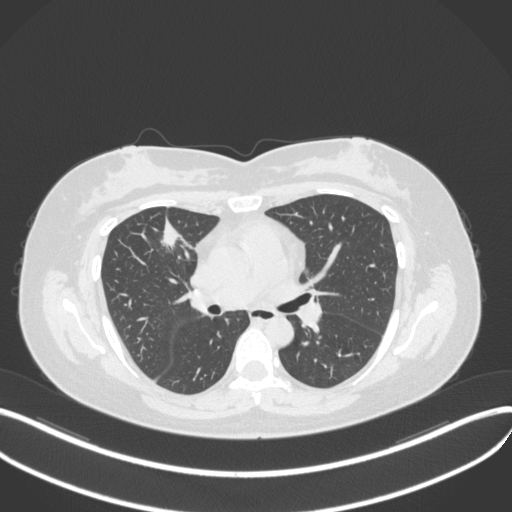
Chest CT, one axial slice. Position 182 of 272 along the scan axis. Reconstruction kernel B31f. 120 kVp. Lung window (W 1500 / L -600 HU). 1 mm slice thickness. 512 × 512 image matrix, field of view 400 × 400 mm. Female patient, age 42 years. Case-level facts recorded for this patient, not image findings: clinical TNM (as recorded): T1b N0 M0.
Outlined on this slice (bounding box drawn by a radiologist):
- lung tumour (recorded histology: adenocarcinoma): bounding box <157,216,189,254> (left, top, right, bottom; pixels)